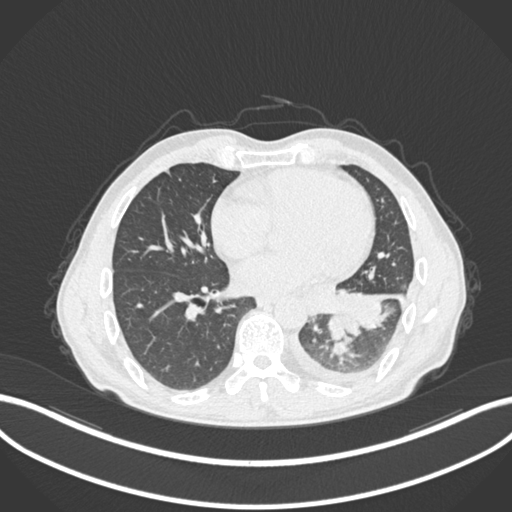
Chest CT, one axial slice; slice 98 of 222 in the series (ordered by position); reconstruction kernel B30f; 120 kVp; lung window (W 1500 / L -600 HU); 1 mm slice thickness; 512 × 512 image matrix. Patient: male, 47 years. From the clinical record (not read from this slice): clinical TNM (as recorded): T3 N1 M1c; histopathological grade: G3.
Outlined on this slice (bounding box drawn by a radiologist):
- lung tumour (recorded histology: small cell carcinoma): bounding box (x1, y1, x2, y2) in pixels: (323, 312, 368, 346)